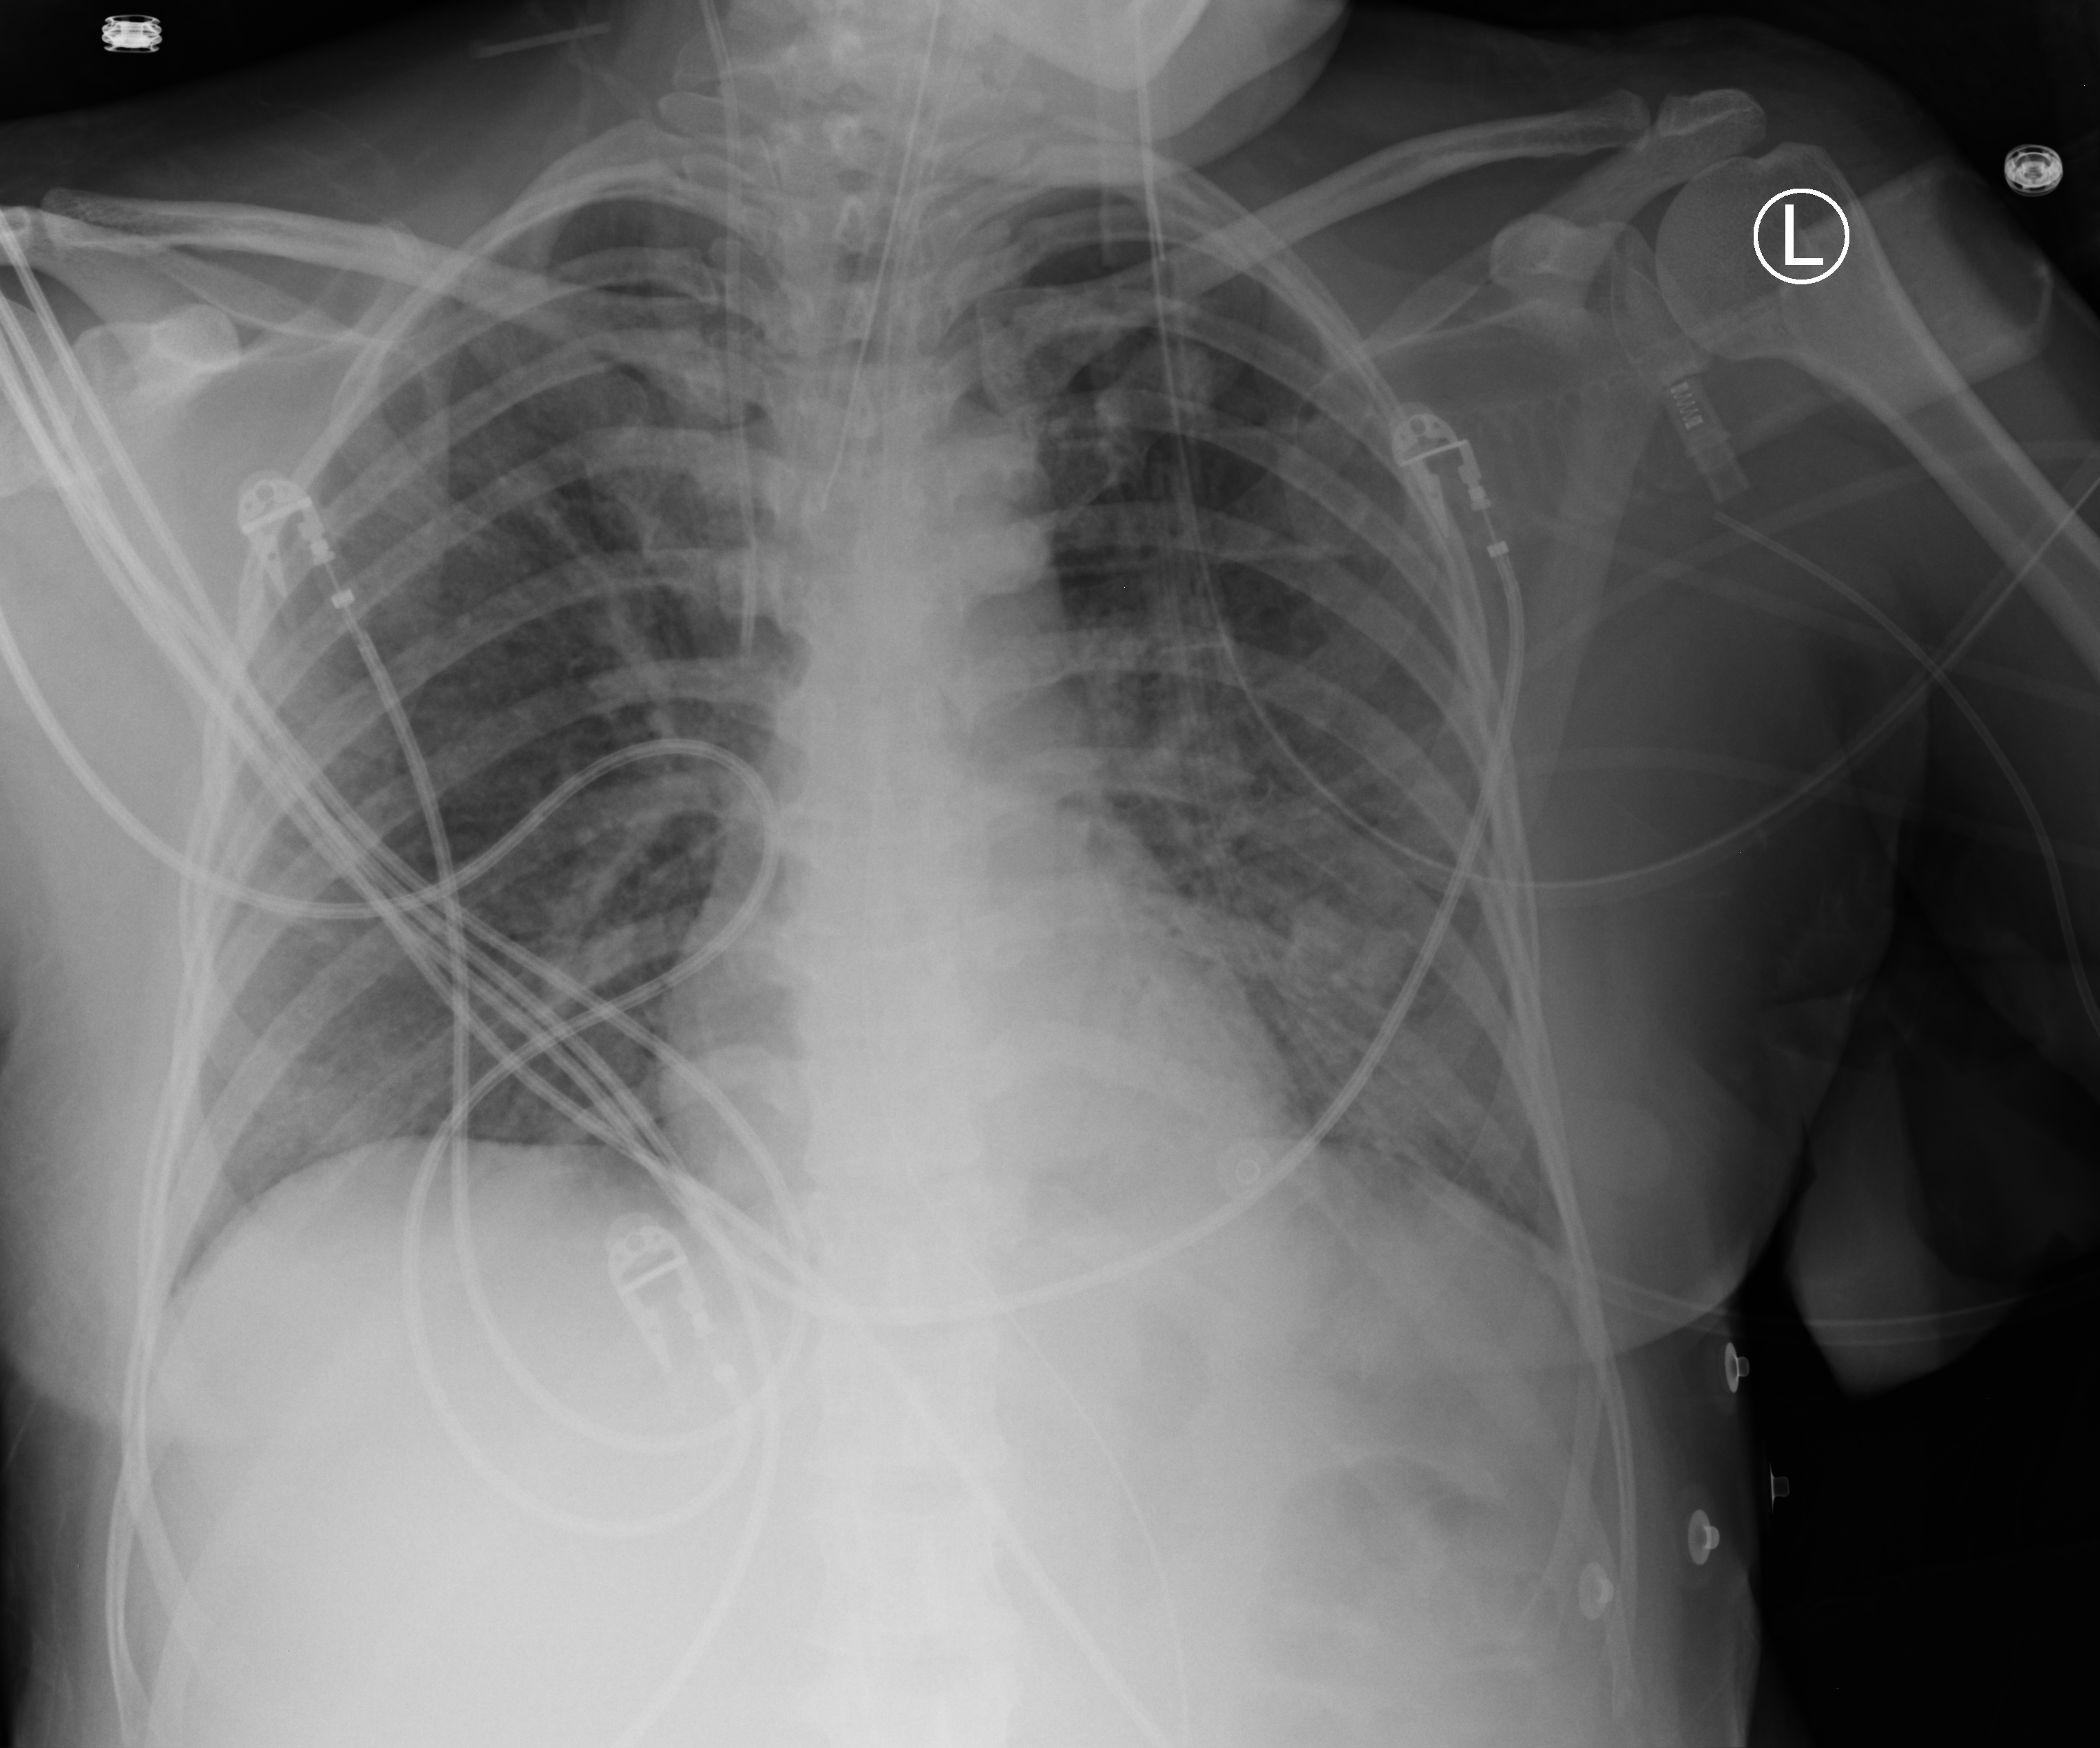
Chest X-ray (portable); anteroposterior (AP) projection. Patient hospitalised with COVID-19; female, aged 18–59 years.
Admission-level facts for this patient (not findings on this image; timing relative to this image not recorded): diabetes (admission record): no.